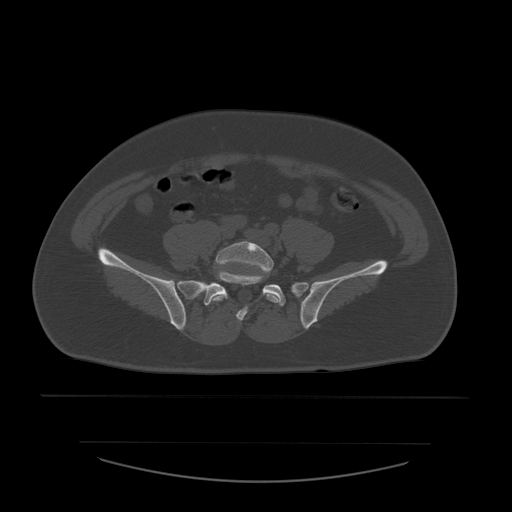
CT including the spine, one axial slice. 120 kVp. Bone window (W 1800 / L 400 HU). 512 × 512 image matrix, field of view 441 × 441 mm. Patient age 44 years. Case-level facts recorded for this patient, not image findings: primary cancer: soft tissue sarcoma.
Outlined on this slice (semi-automatically segmented with operator editing):
- L5 vertebra: bounding box <212,241,280,304> (left, top, right, bottom; pixels)